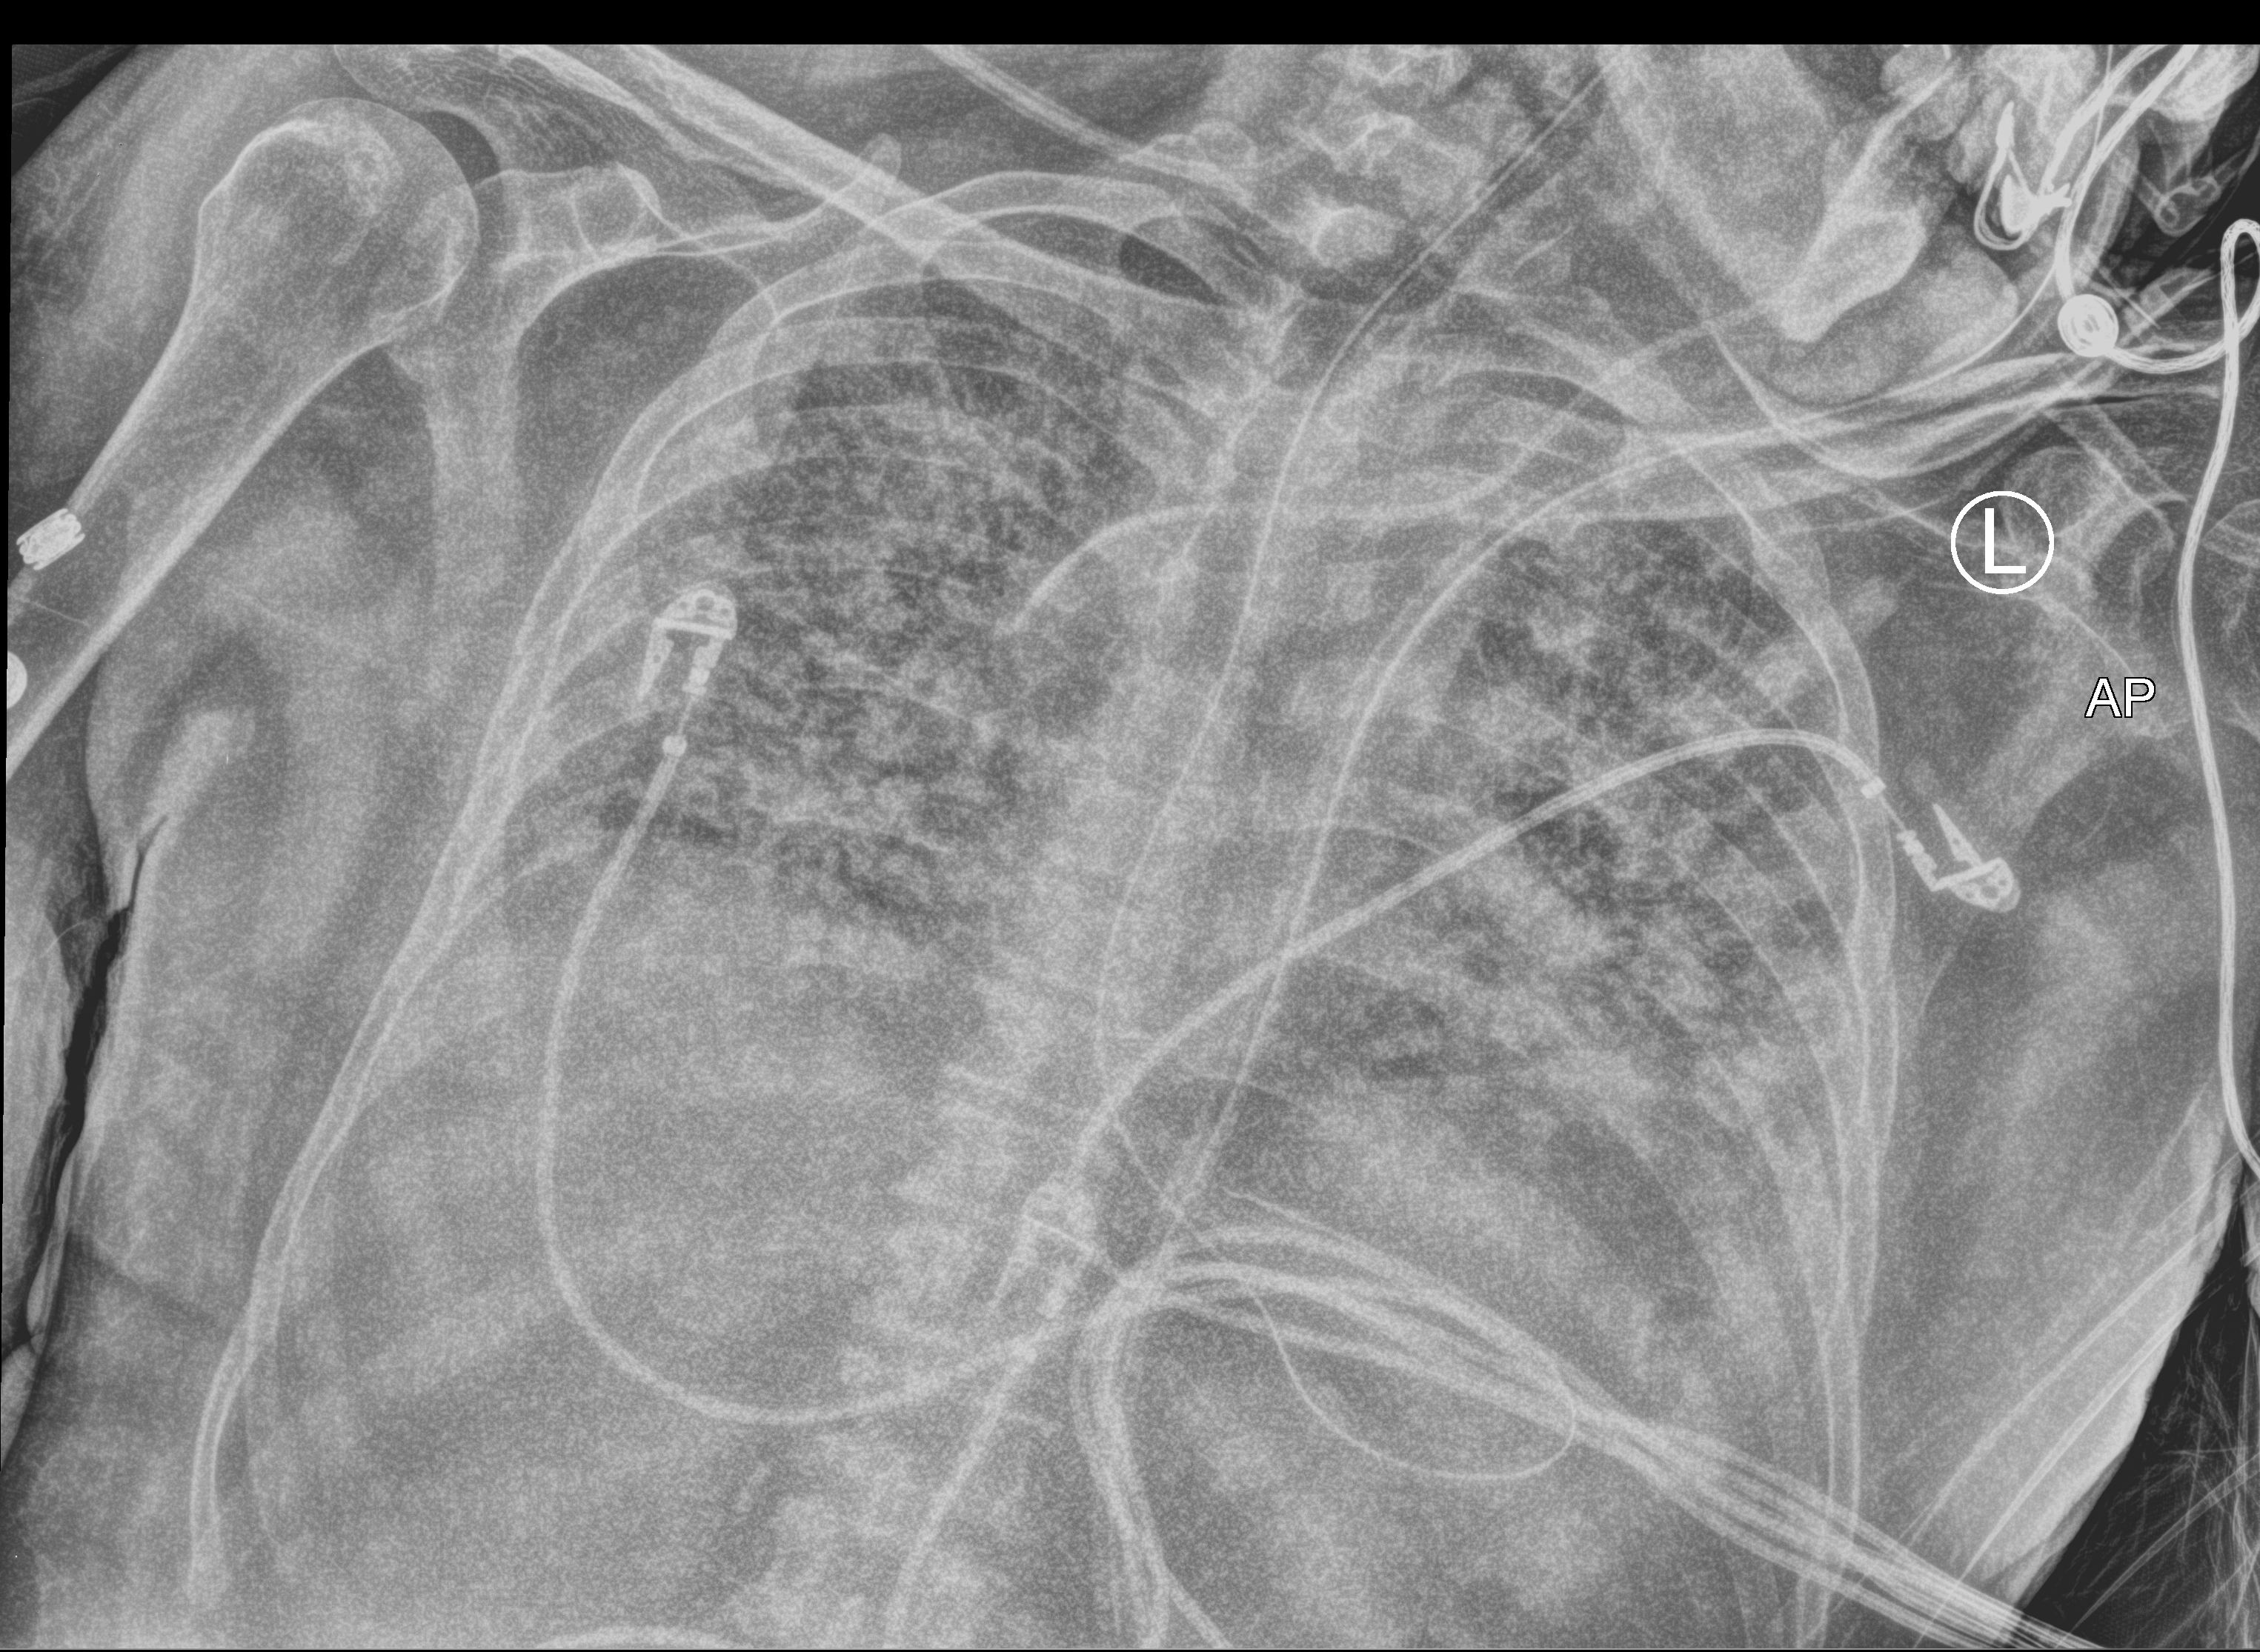
Chest X-ray (portable), anteroposterior (AP) projection. Male patient hospitalised with COVID-19, age 60–74 years.
Admission-level facts for this patient (not findings on this image; timing relative to this image not recorded): diabetes (admission record): no; mechanically ventilated during this hospital stay: yes; chronic kidney disease (admission record): no.